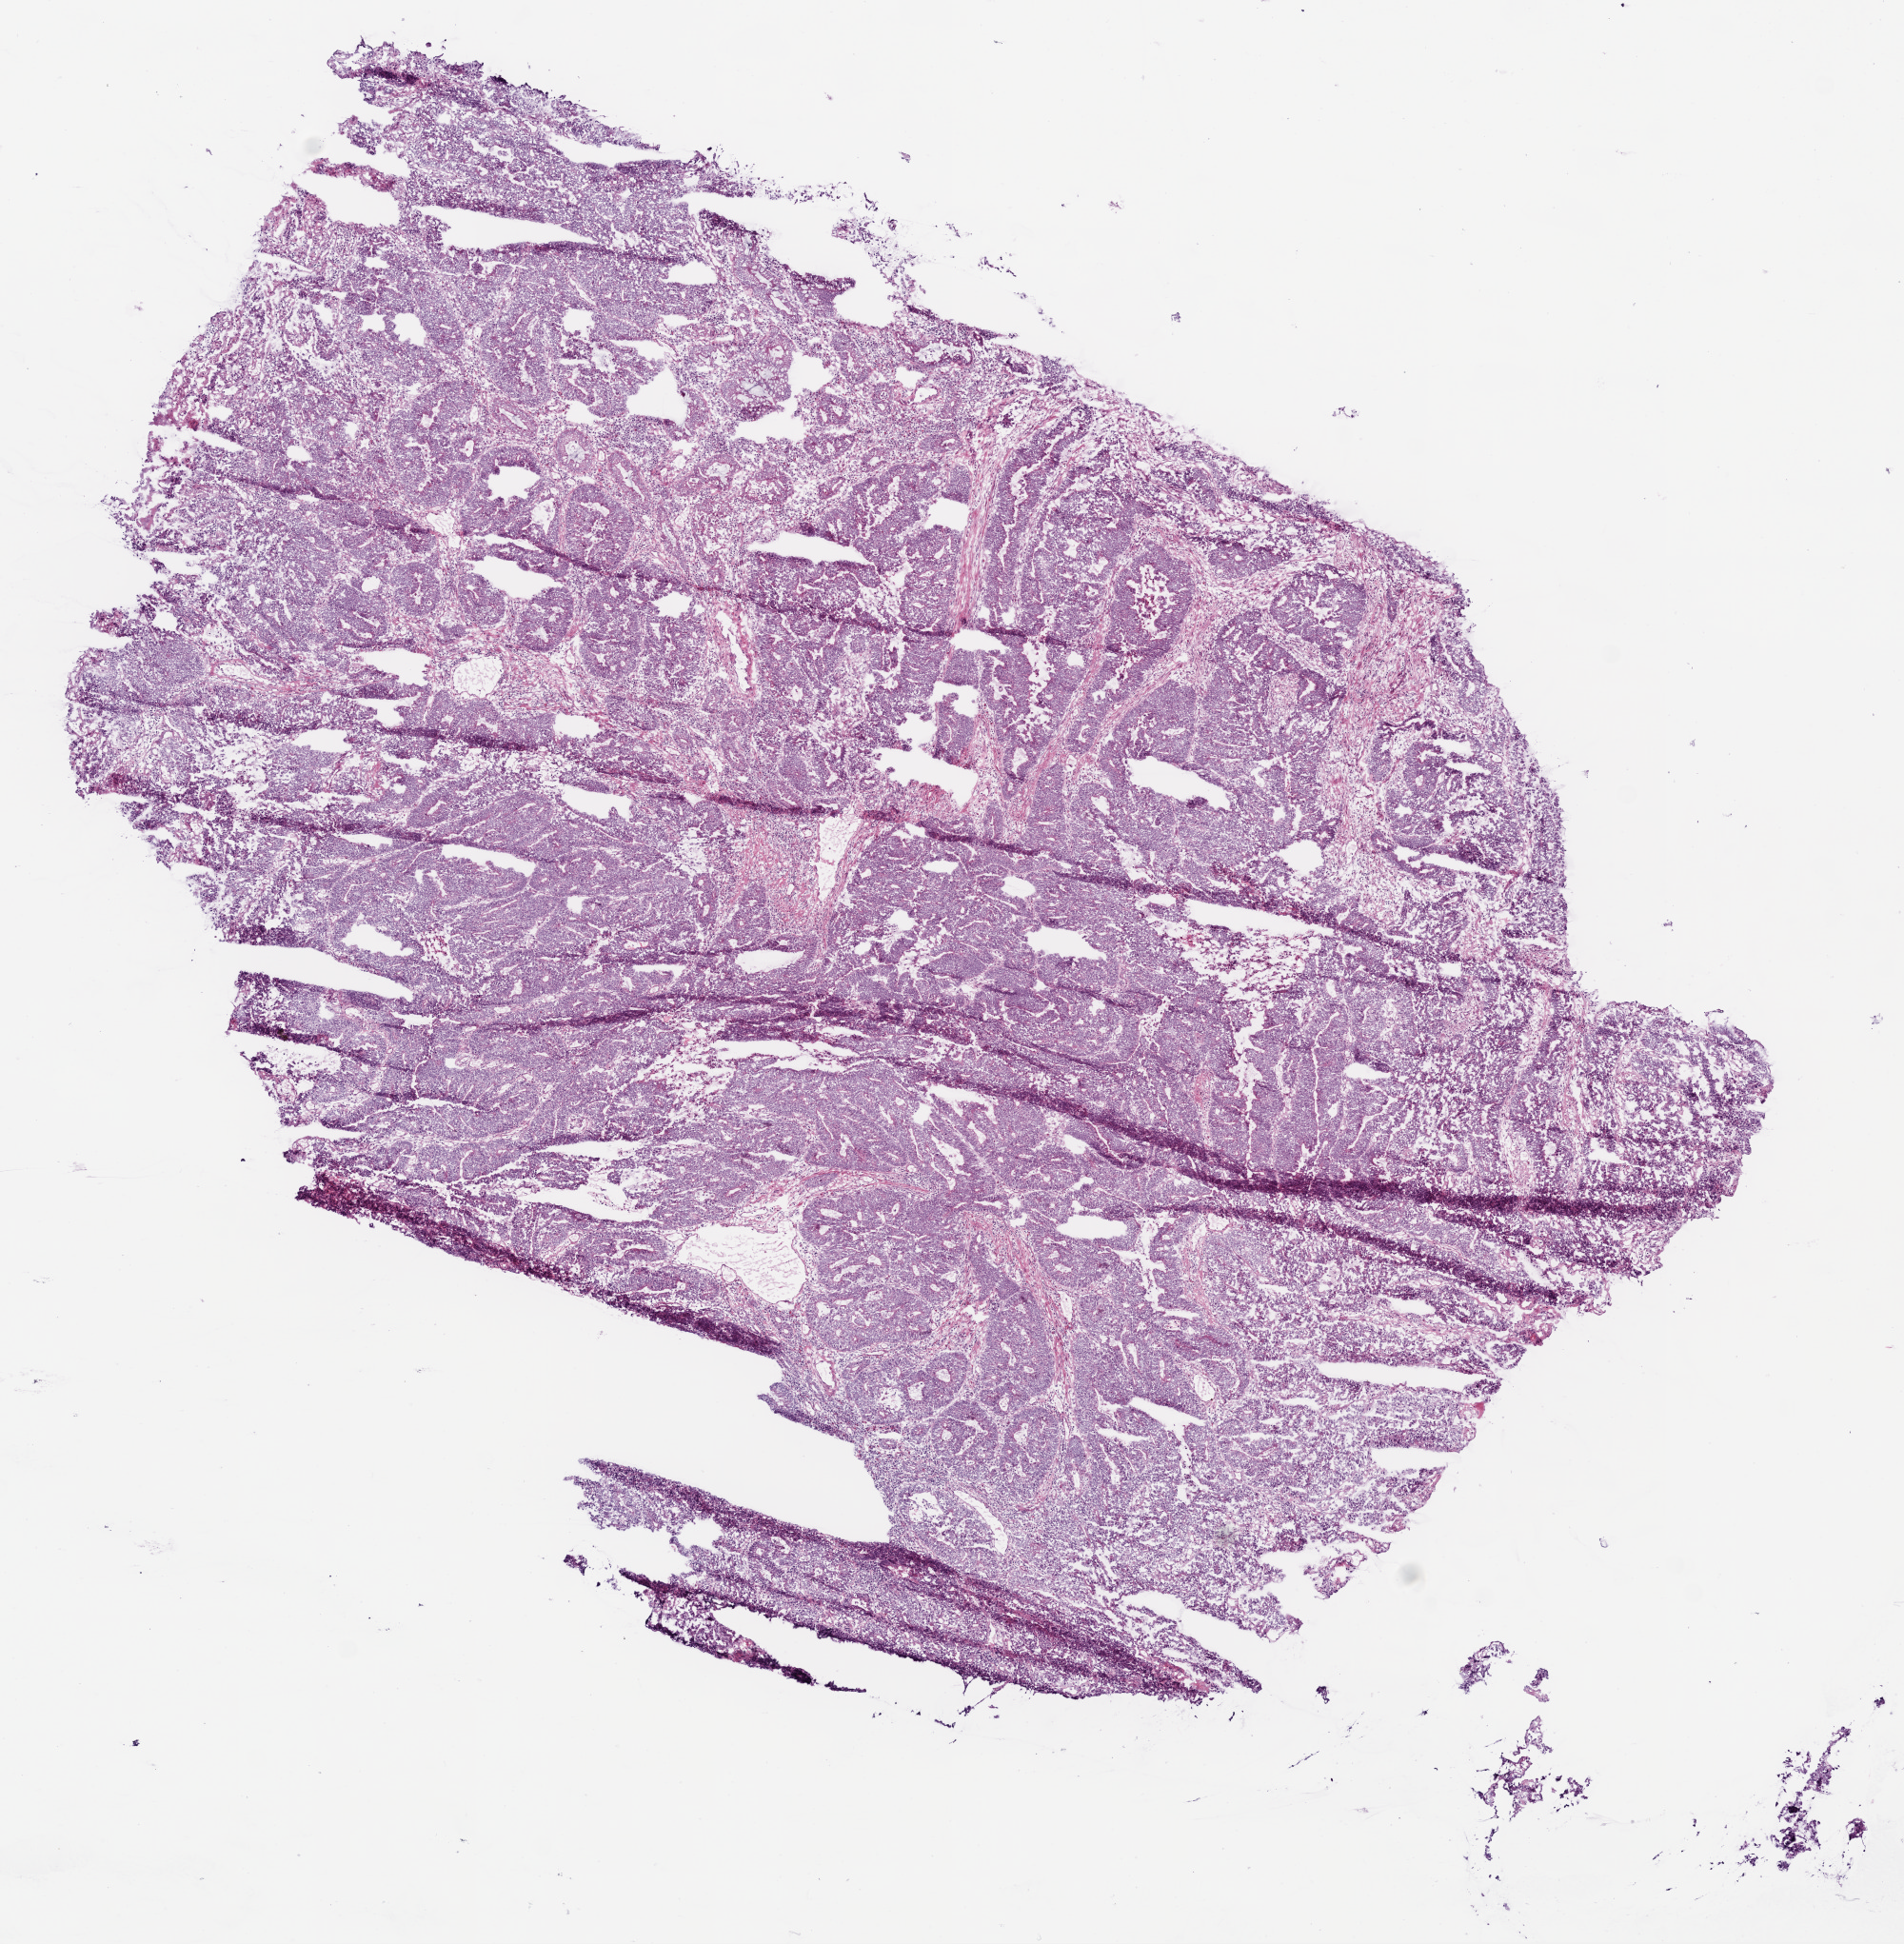
Digitized H&E tissue section (whole slide) — low-resolution overview of the scanned area, about 8.0 x 8.2 mm (acquisition: 20x scan), frozen section from the bottom of the tissue portion, rectum, primary tumour sample. Male, age 68 years at initial diagnosis. Slide review estimates, as recorded: tumour cells 82%, tumour nuclei 80%, normal cells 0%, stromal cells 8%, necrosis 10%.
* lymph nodes positive (case pathology): 0 of 14 examined
* AJCC pathologic stage: IIA (6th edition)
* diagnosis: Mucinous adenocarcinoma
* TNM: T3 N0 M0